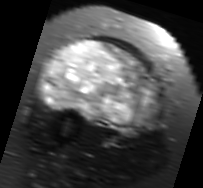
MRI of an extremity soft-tissue mass, one axial slice; slice 37 of 91 in the series (ordered by position); T2-weighted fat-saturated; MR volume resampled by the dataset authors to the PET/CT grid (not the native acquisition matrix); 3.27 mm slice thickness; 203 × 188 image matrix, field of view 198 × 184 mm. Female patient. Case-level facts recorded for this patient, not image findings: histological type: malignant solitary fibrous tumor; grade: intermediate; site of the primary tumour: right thigh.
Structures marked on this image (expert contour drawn on MRI and transferred to this co-registered scan by the dataset authors):
- gross tumour volume including surrounding oedema: bounding box <37,38,162,134> (left, top, right, bottom; pixels)
- gross tumour volume (mass): <42,40,157,130>